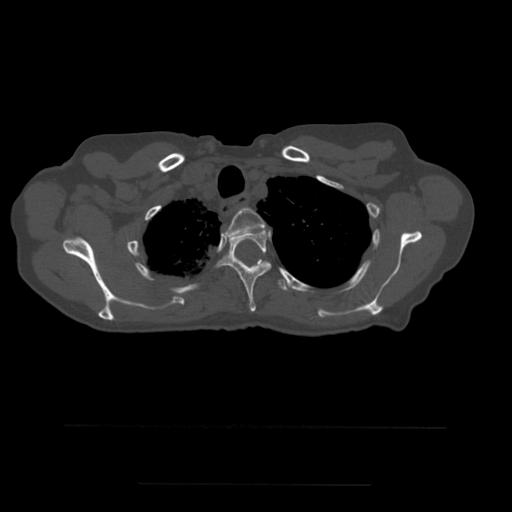
CT including the spine, one axial slice; slice 422 of 544 in the series (ordered by position); bone window (W 1800 / L 400 HU); 1.25 mm slice thickness; 512 × 512 image matrix, field of view 350 × 350 mm. Patient age 58 years. Case-level facts recorded for this patient, not image findings: primary cancer: lung.
Annotated regions visible in this slice (semi-automatic segmentation, software-assisted and operator-edited):
- T2 vertebra: box from (x=223, y=208) to (x=266, y=240) px
- T3 vertebra: (x=217, y=230)–(x=272, y=312)
- T4 vertebra: (x=246, y=265)–(x=289, y=291)